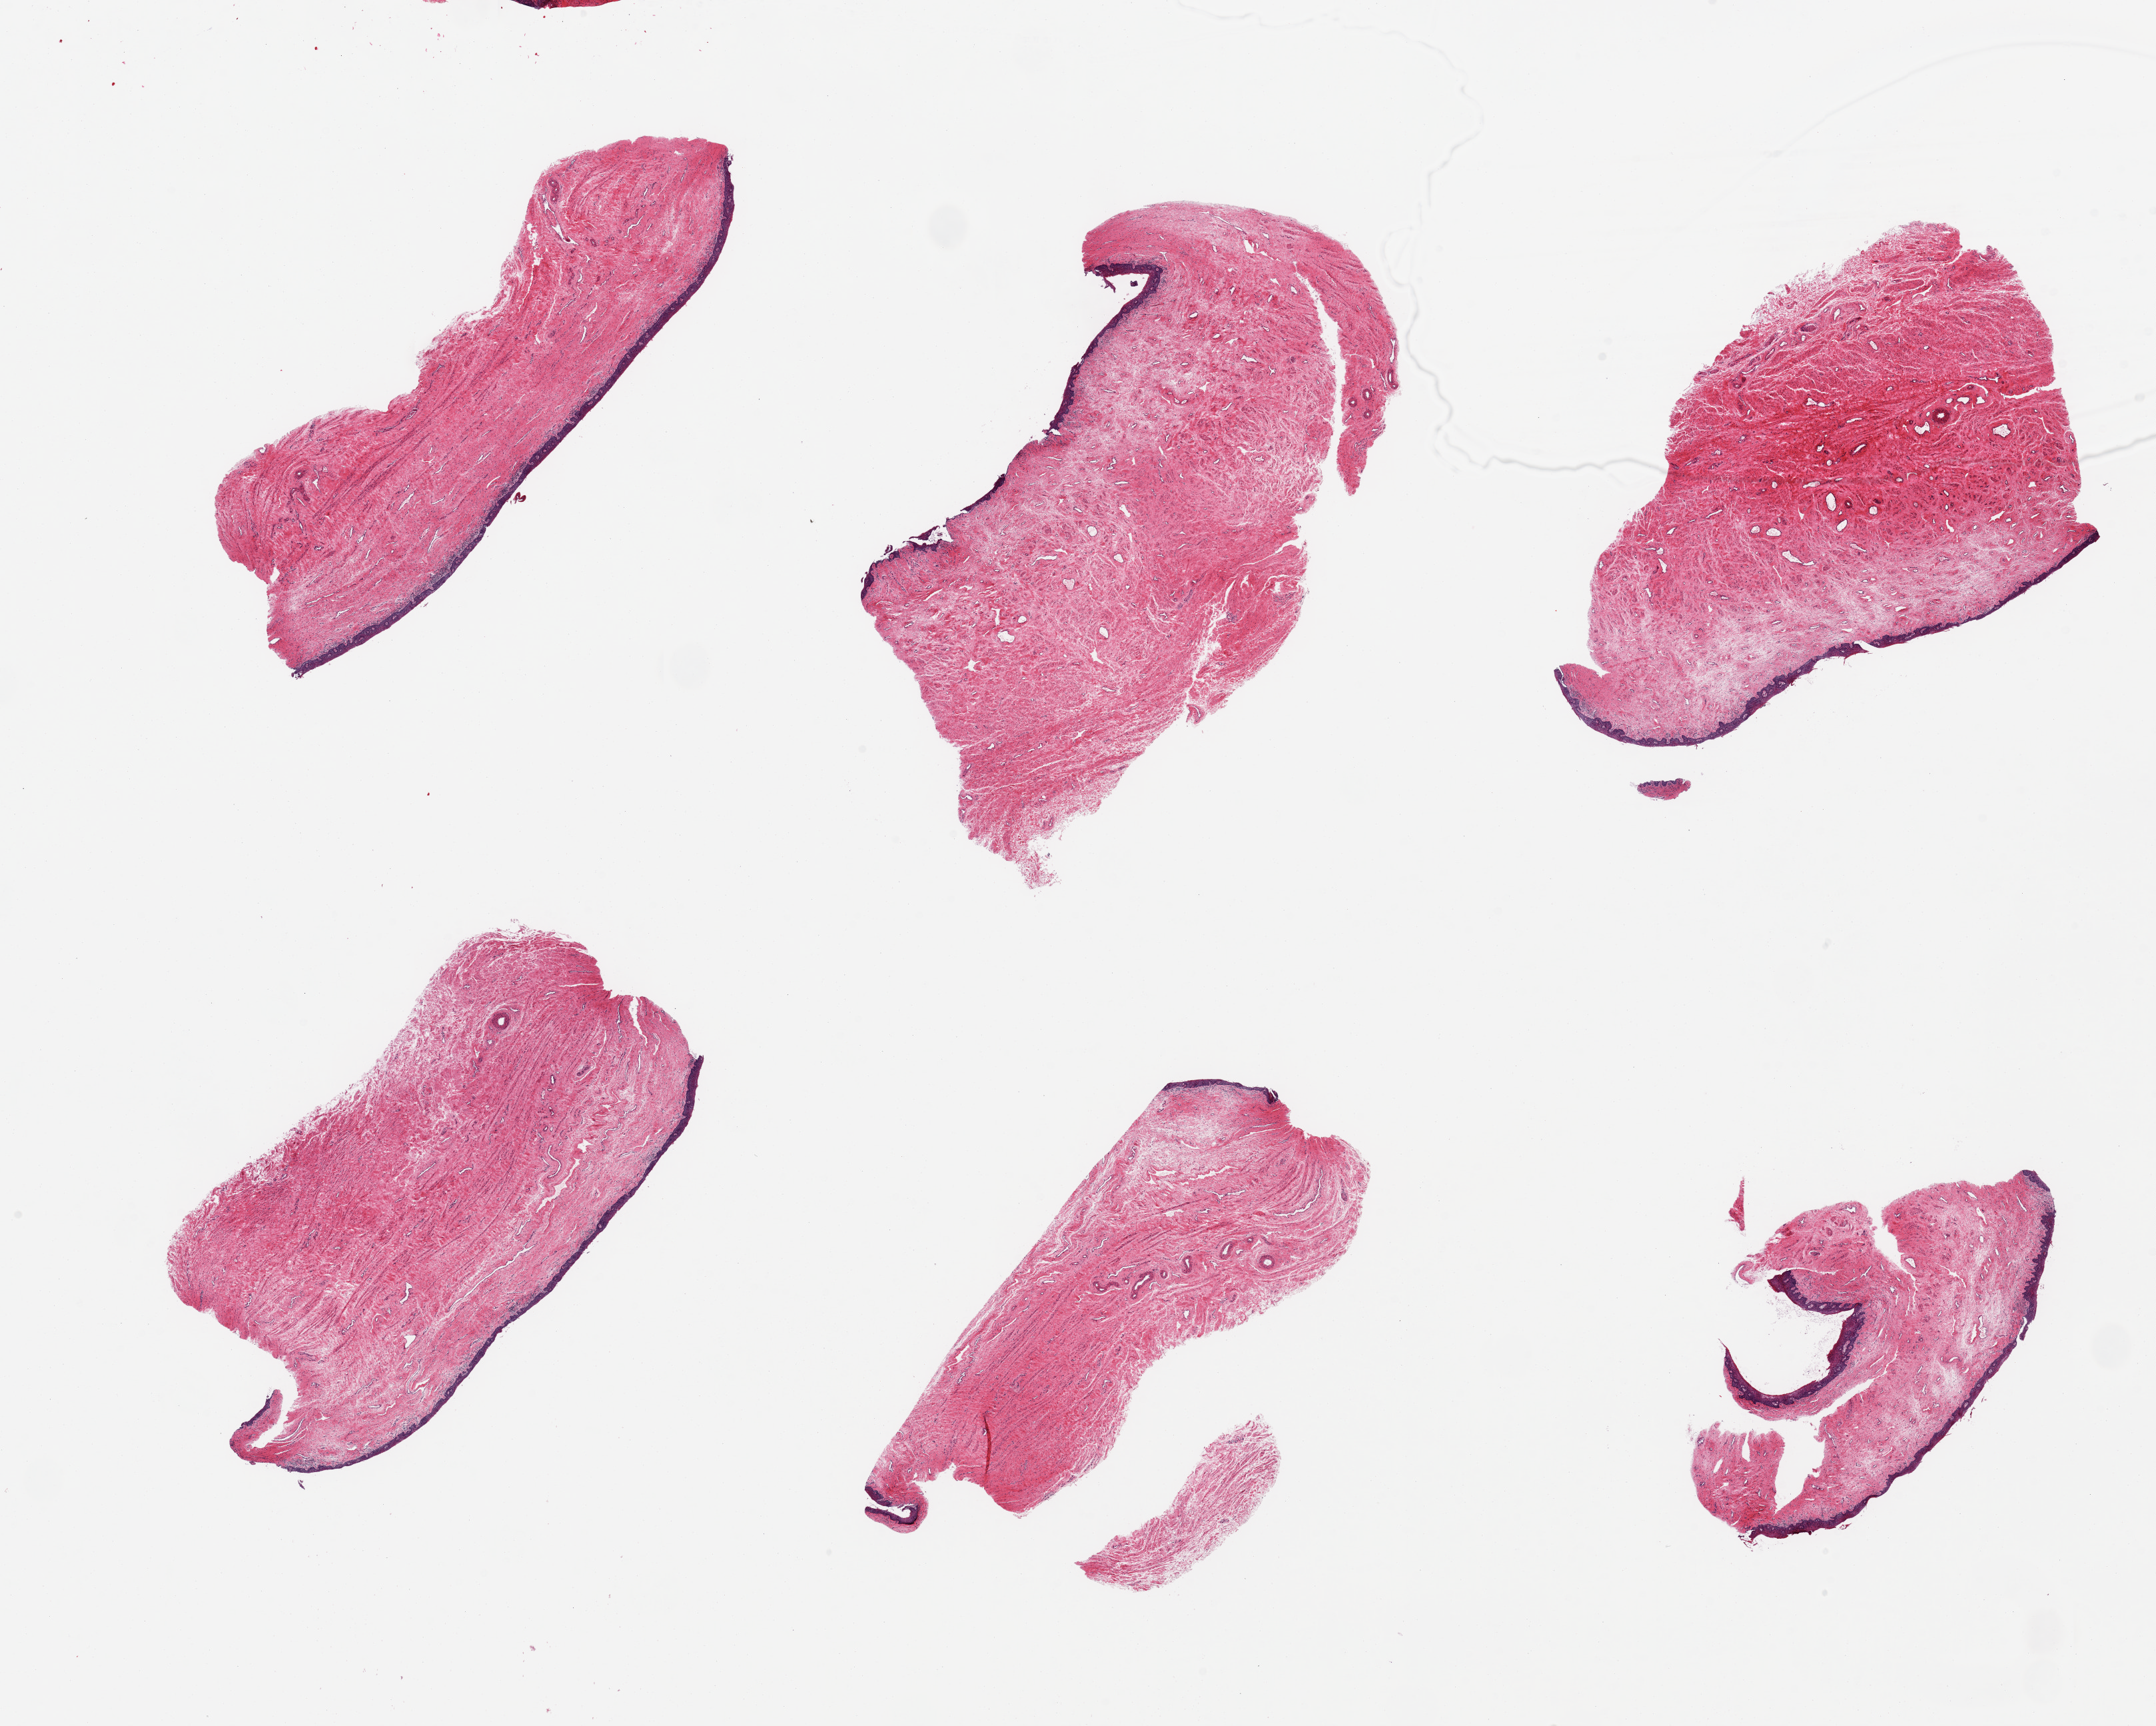
Haematoxylin and eosin whole-slide image — whole scanned area (about 25.6 x 20.5 mm, from a 20x scan) shown as a low-resolution overview. PAXgene-fixed, paraffin-embedded tissue. Section of vagina (target tissue). Tissue donor sample. Donor sex: female.
Reviewer comment on this tissue sample: 6 pieces; chronic inflammation.